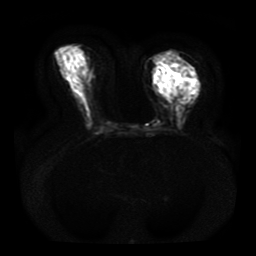
Breast MRI, one axial slice. Position 18 of 41 along the scan axis. Diffusion-weighted series; image 2 of 4 stored at this slice position (different b-values; order by instance number). 1.5 T. 5 mm slice thickness. 256 × 256 image matrix, field of view 330 × 330 mm. Female patient.
Annotated regions visible in this slice (outlined manually by an expert reader):
- tumour on diffusion-weighted imaging: bounding box (x1, y1, x2, y2) in pixels: (182, 83, 186, 87)